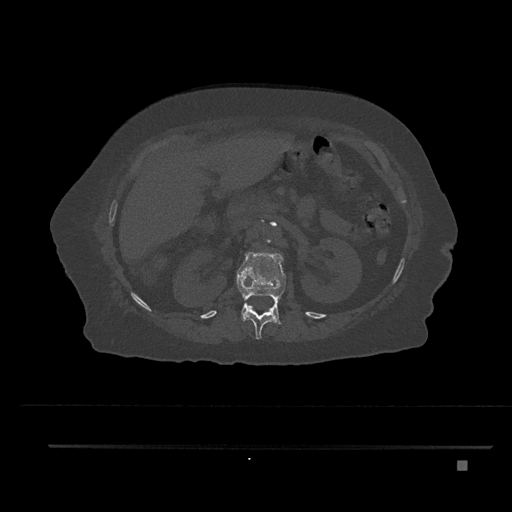
CT including the spine, one axial slice. Slice 238 of 797 in the series (ordered by position). Bone window (W 1800 / L 400 HU). 0.5 mm slice thickness. 512 × 512 image matrix. Patient: female, 76 years. Case-level facts recorded for this patient, not image findings: primary cancer: lung.
Annotated regions visible in this slice (semi-automatically segmented with operator editing):
- L1 vertebra: bounding box [x1, y1, x2, y2] px = [236, 250, 286, 324]
- T12 vertebra: [245, 306, 275, 339]